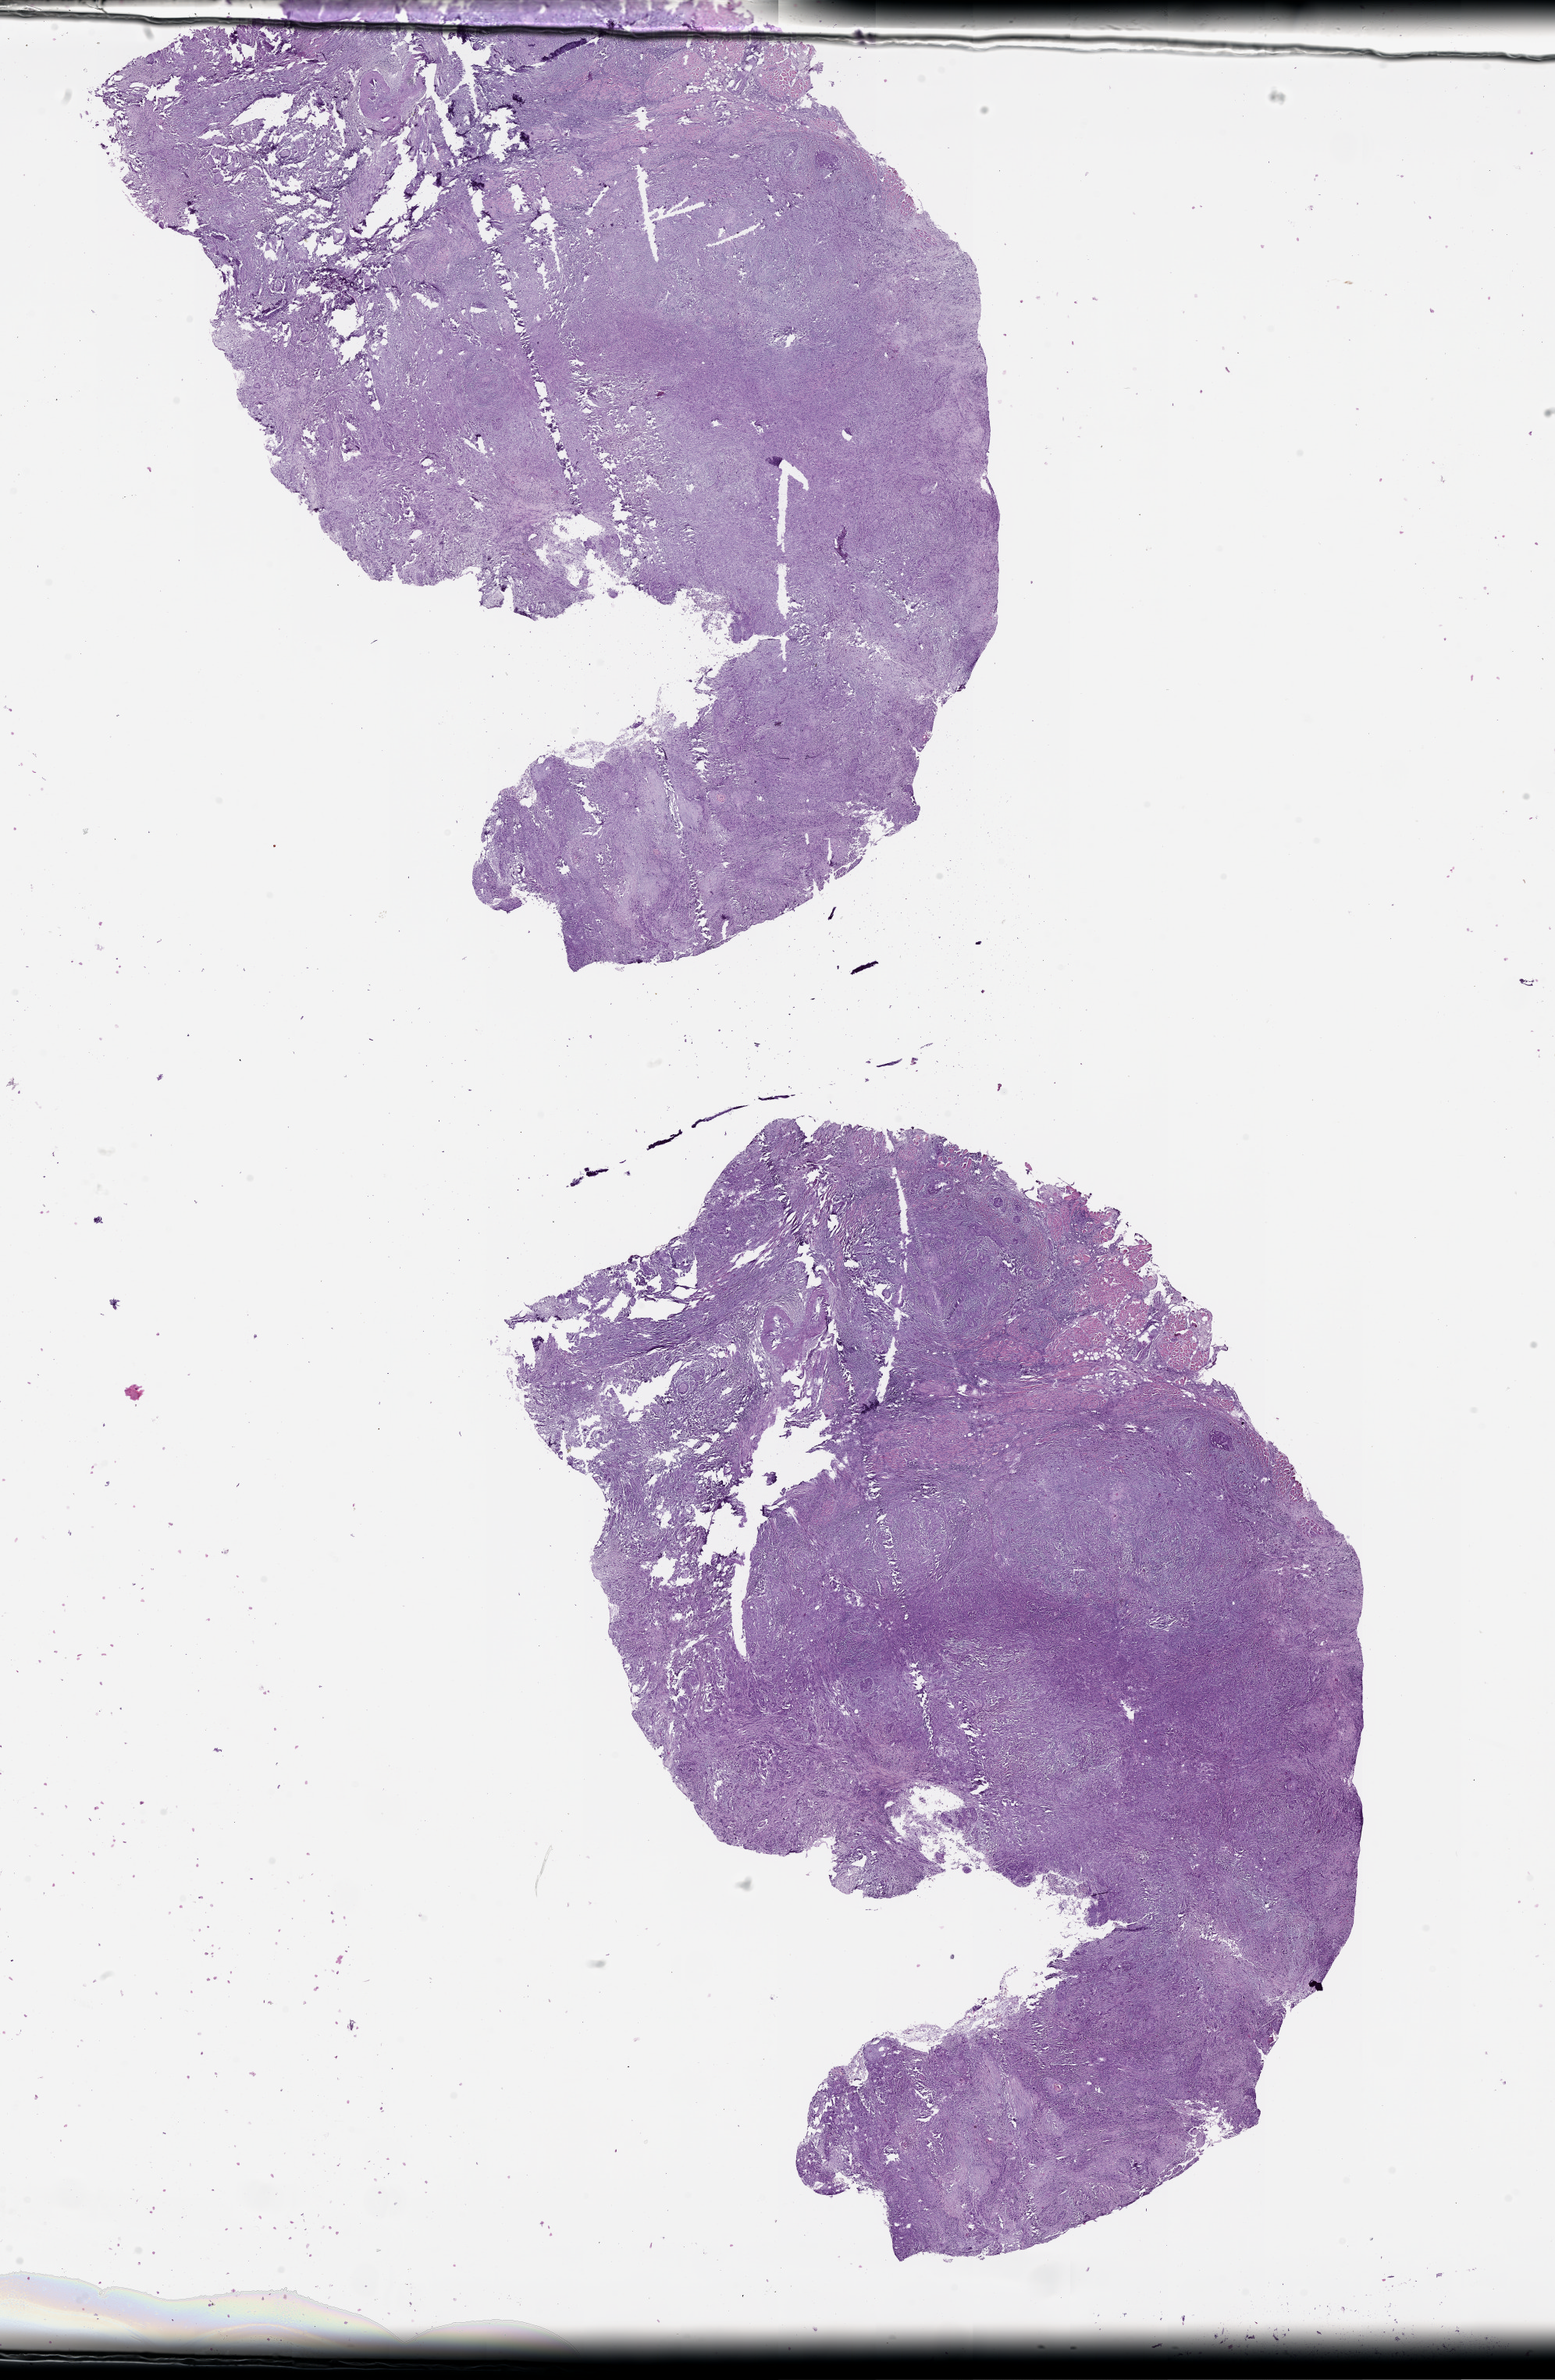
Whole-slide histology image, Hematoxylin and eosin (H&E) stained — shown as a low-resolution overview of the whole scanned area (about 16.0 x 24.5 mm). Head and neck, tissue type not recorded.
- patient diagnosis (cohort enrolment): head and neck cancer (head-neck)